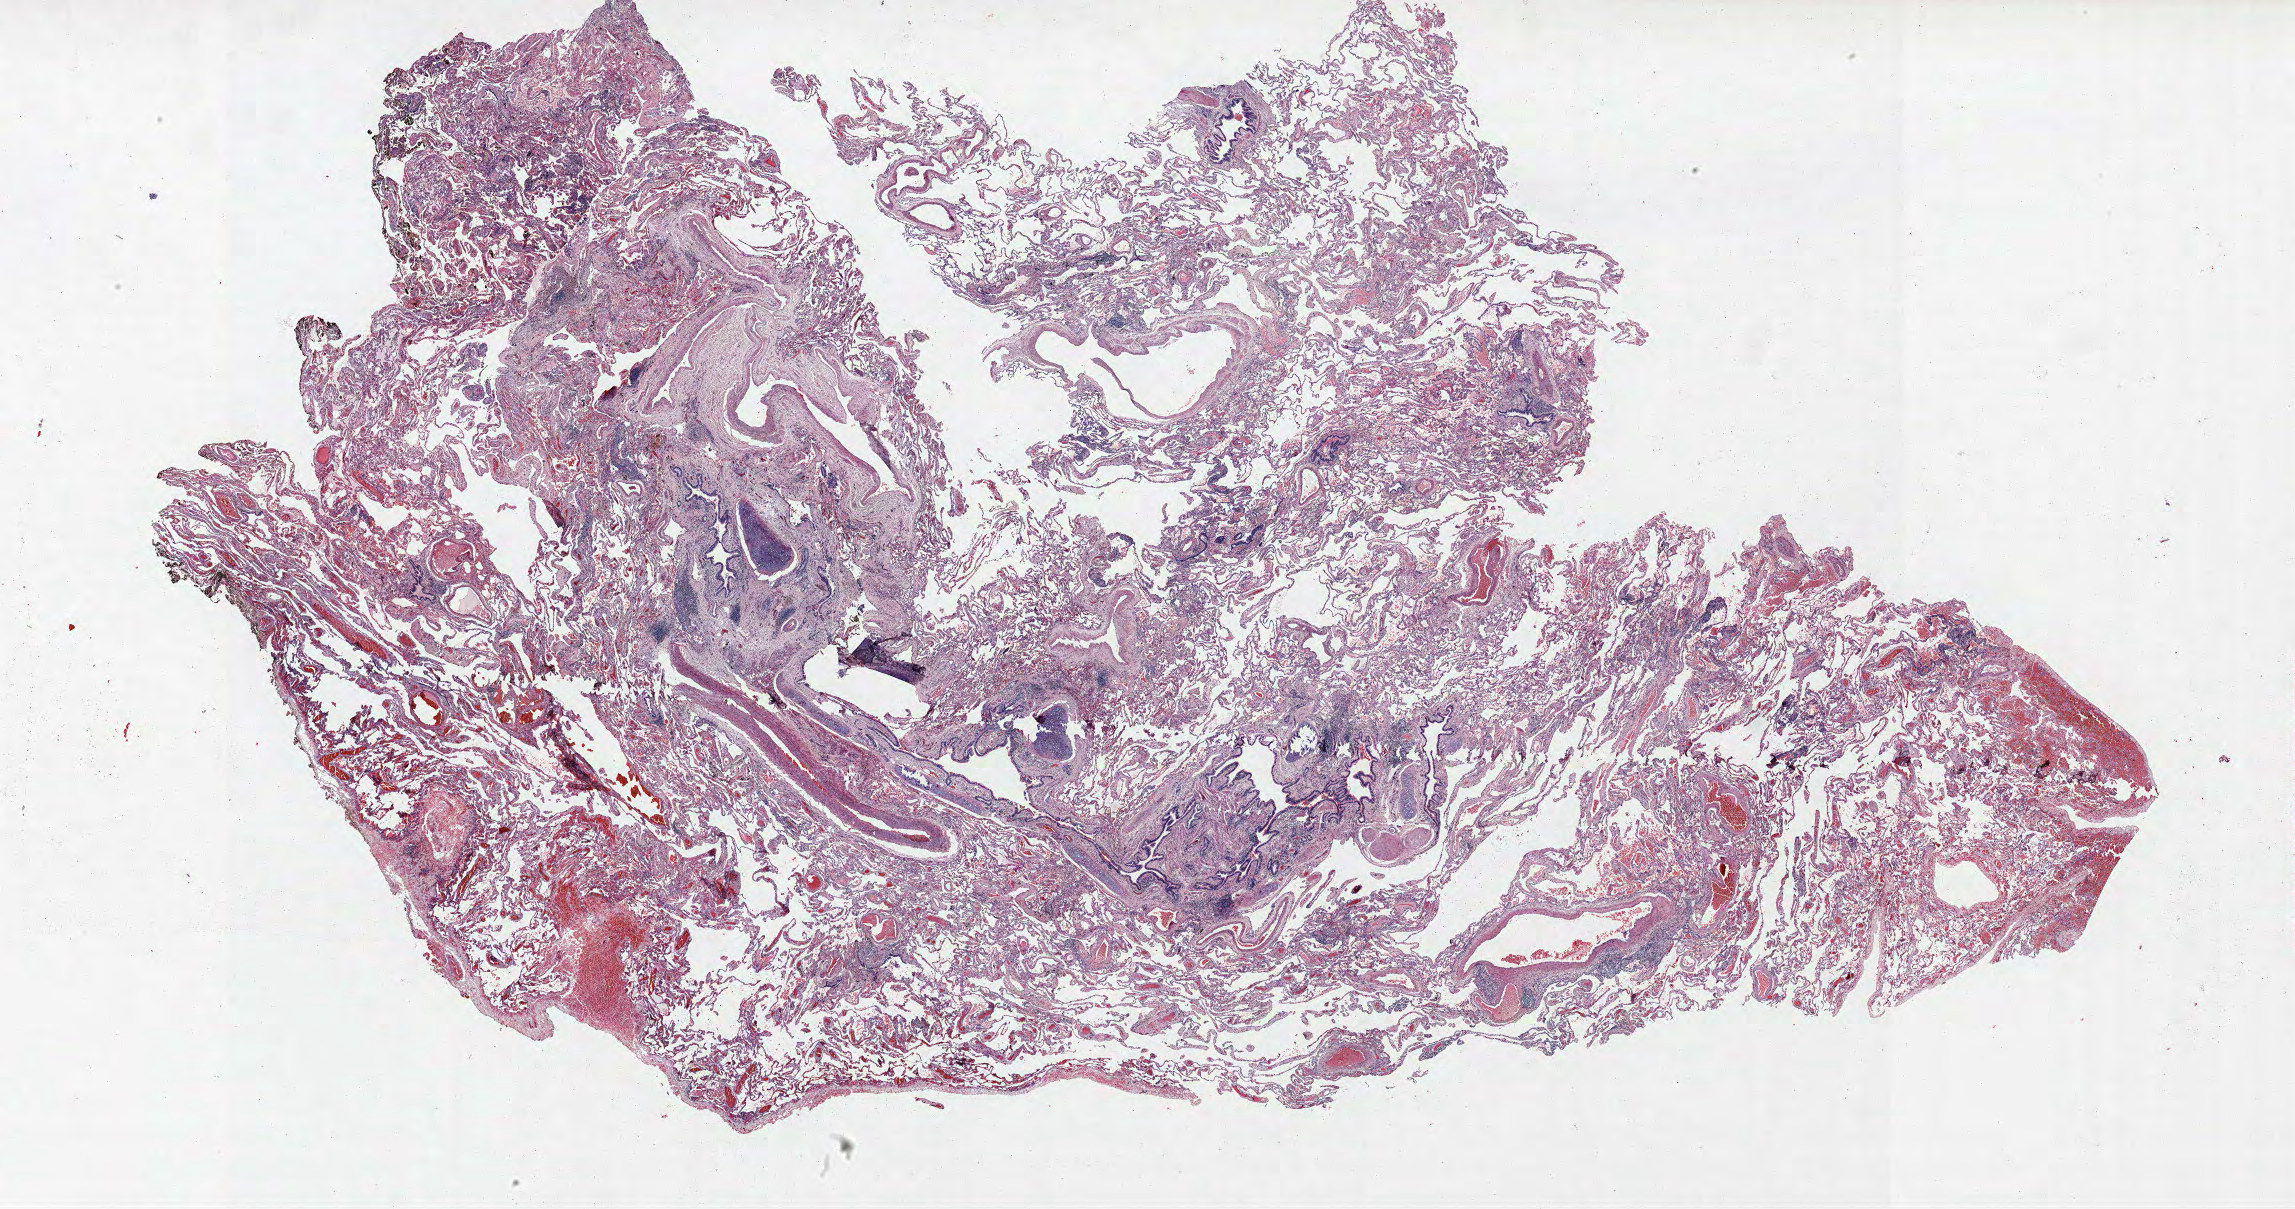
Whole-slide histology image, Hematoxylin and eosin (H&E) stained, a low-resolution overview of the entire scanned area, about 36.7 x 19.3 mm, formalin-fixed paraffin-embedded (FFPE) section, lung. Female patient, aged 59 at enrolment. Current smoker at enrolment. Grade: moderately differentiated (G2).
- tumour size (pathology): 11 mm
- participant's lung-cancer diagnosis: Adenocarcinoma, NOS
- stage (AJCC 6th edition): IA
- primary tumour location (clinical record): right middle lobe
- note: participant had 2 primary lung cancers recorded; fields above describe the first